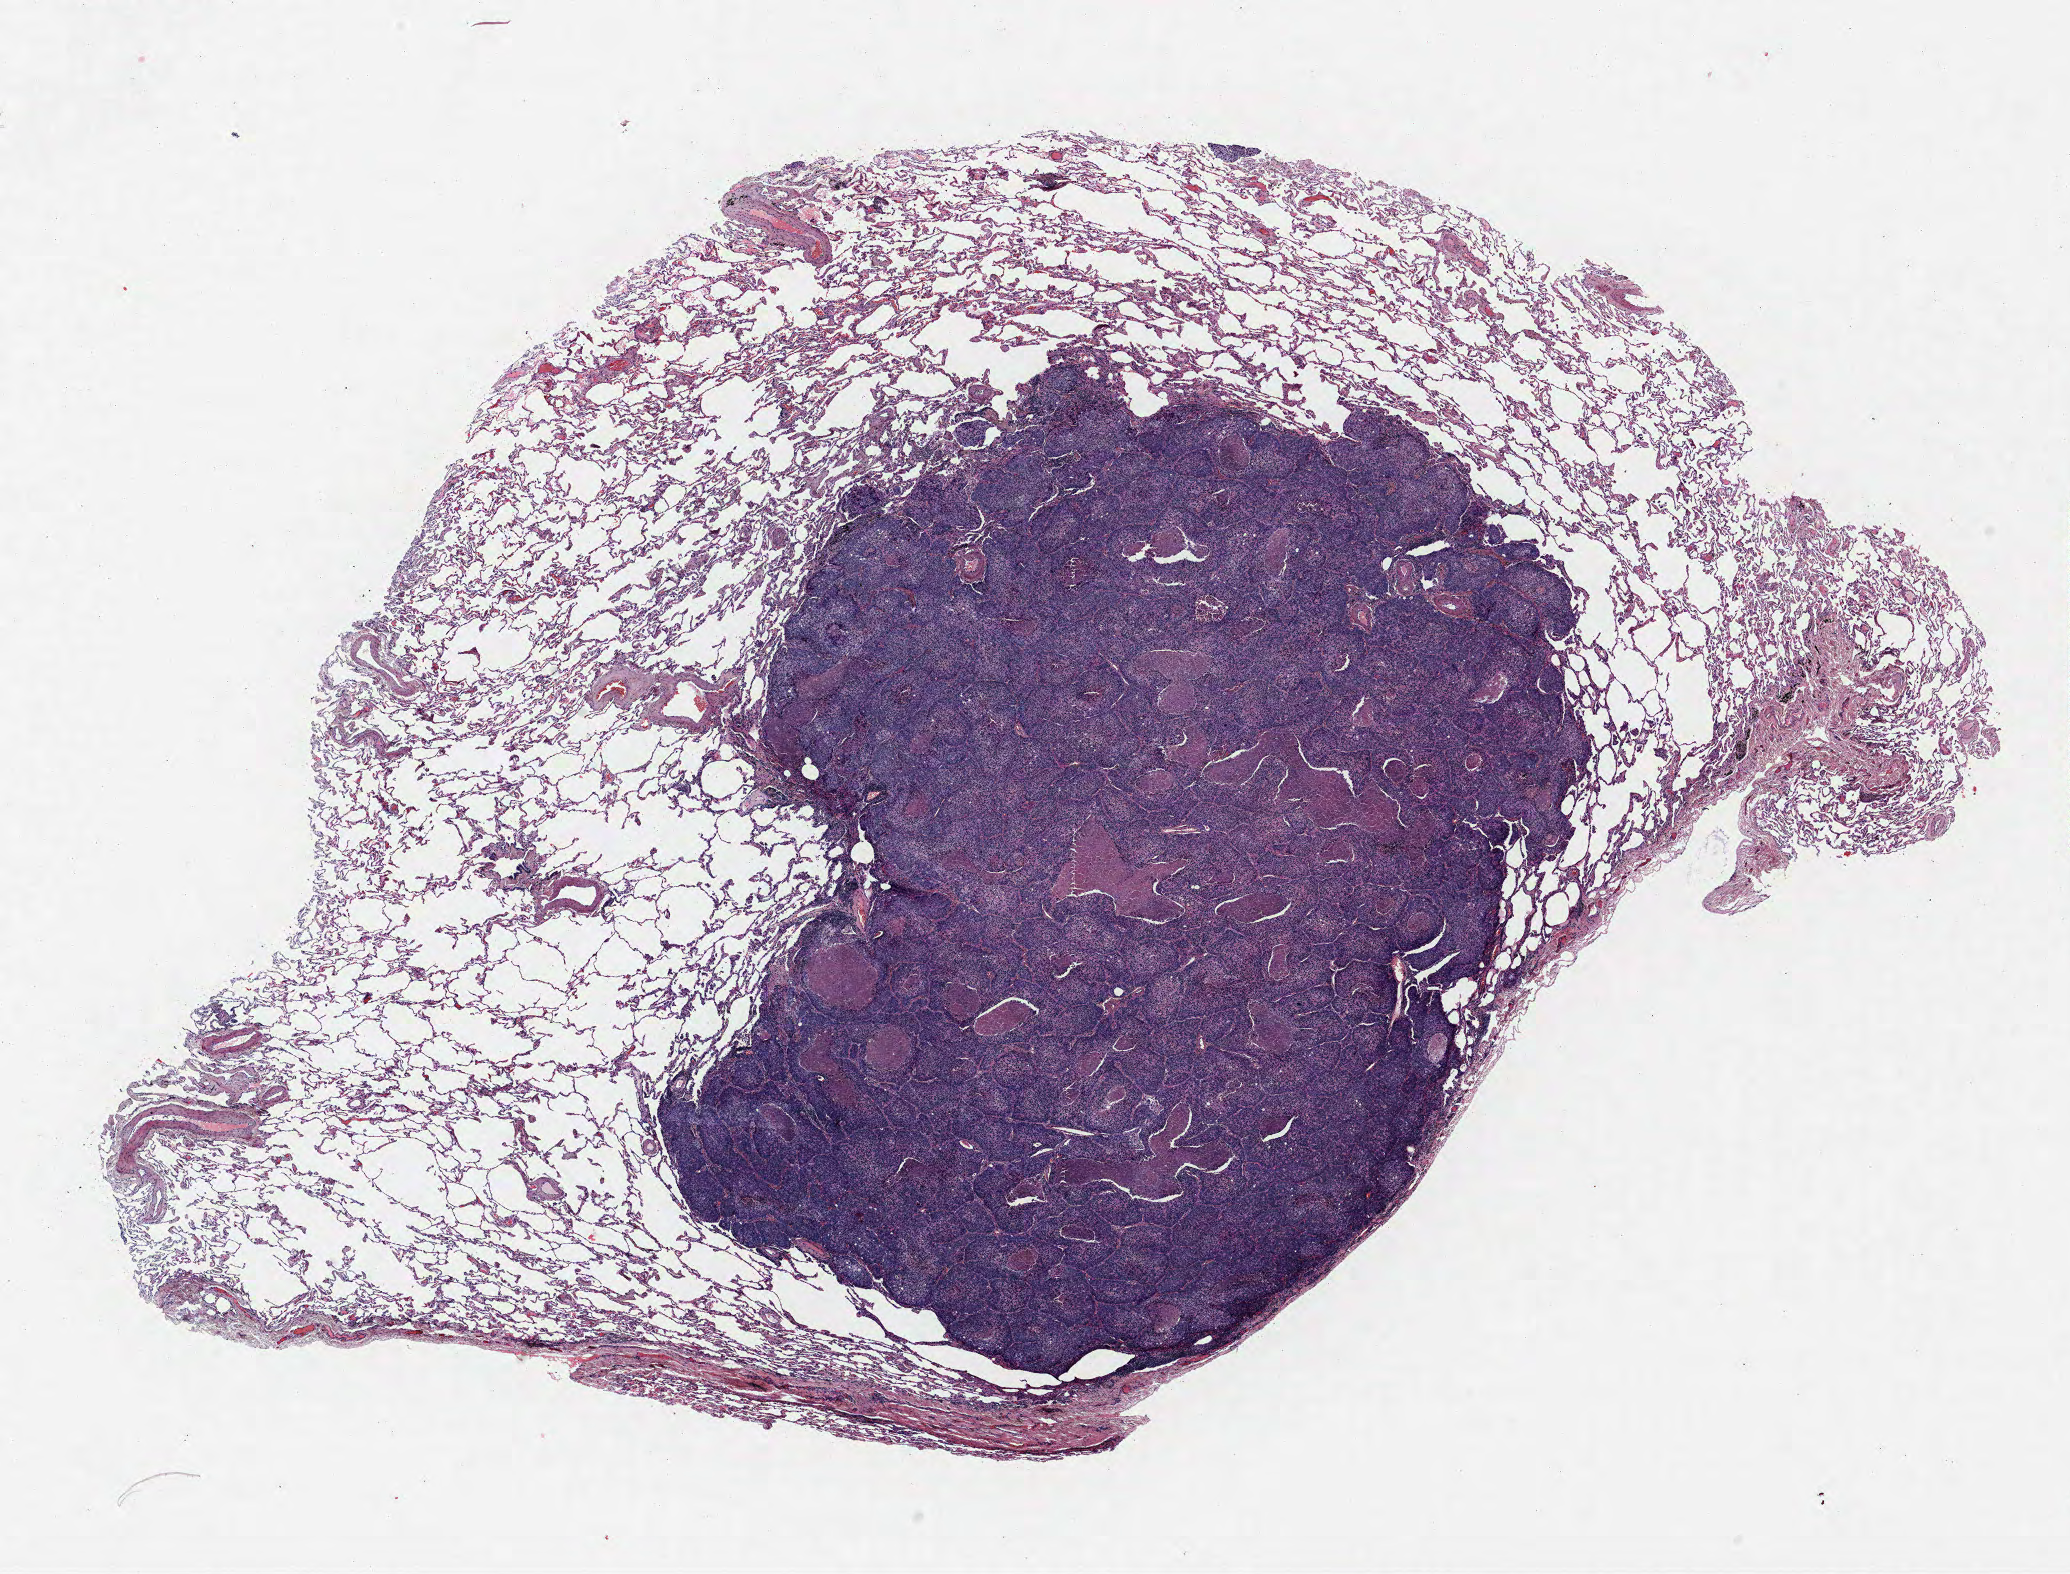
H&E whole-slide image, low-resolution overview of the scanned area, about 16.6 x 12.6 mm (from a 40x scan), formalin-fixed paraffin-embedded (FFPE) section, lung tissue. Male patient, aged 64 at enrolment. Former smoker at enrolment. Grade: poorly differentiated (G3).
Tumour size (pathology): 14 mm. ICD-O-3 topography: upper lobe of lung (C34.1). Primary tumour location (clinical record): left upper lobe. Participant's lung-cancer diagnosis: Squamous cell carcinoma, NOS. Stage (AJCC 6th edition): IA.